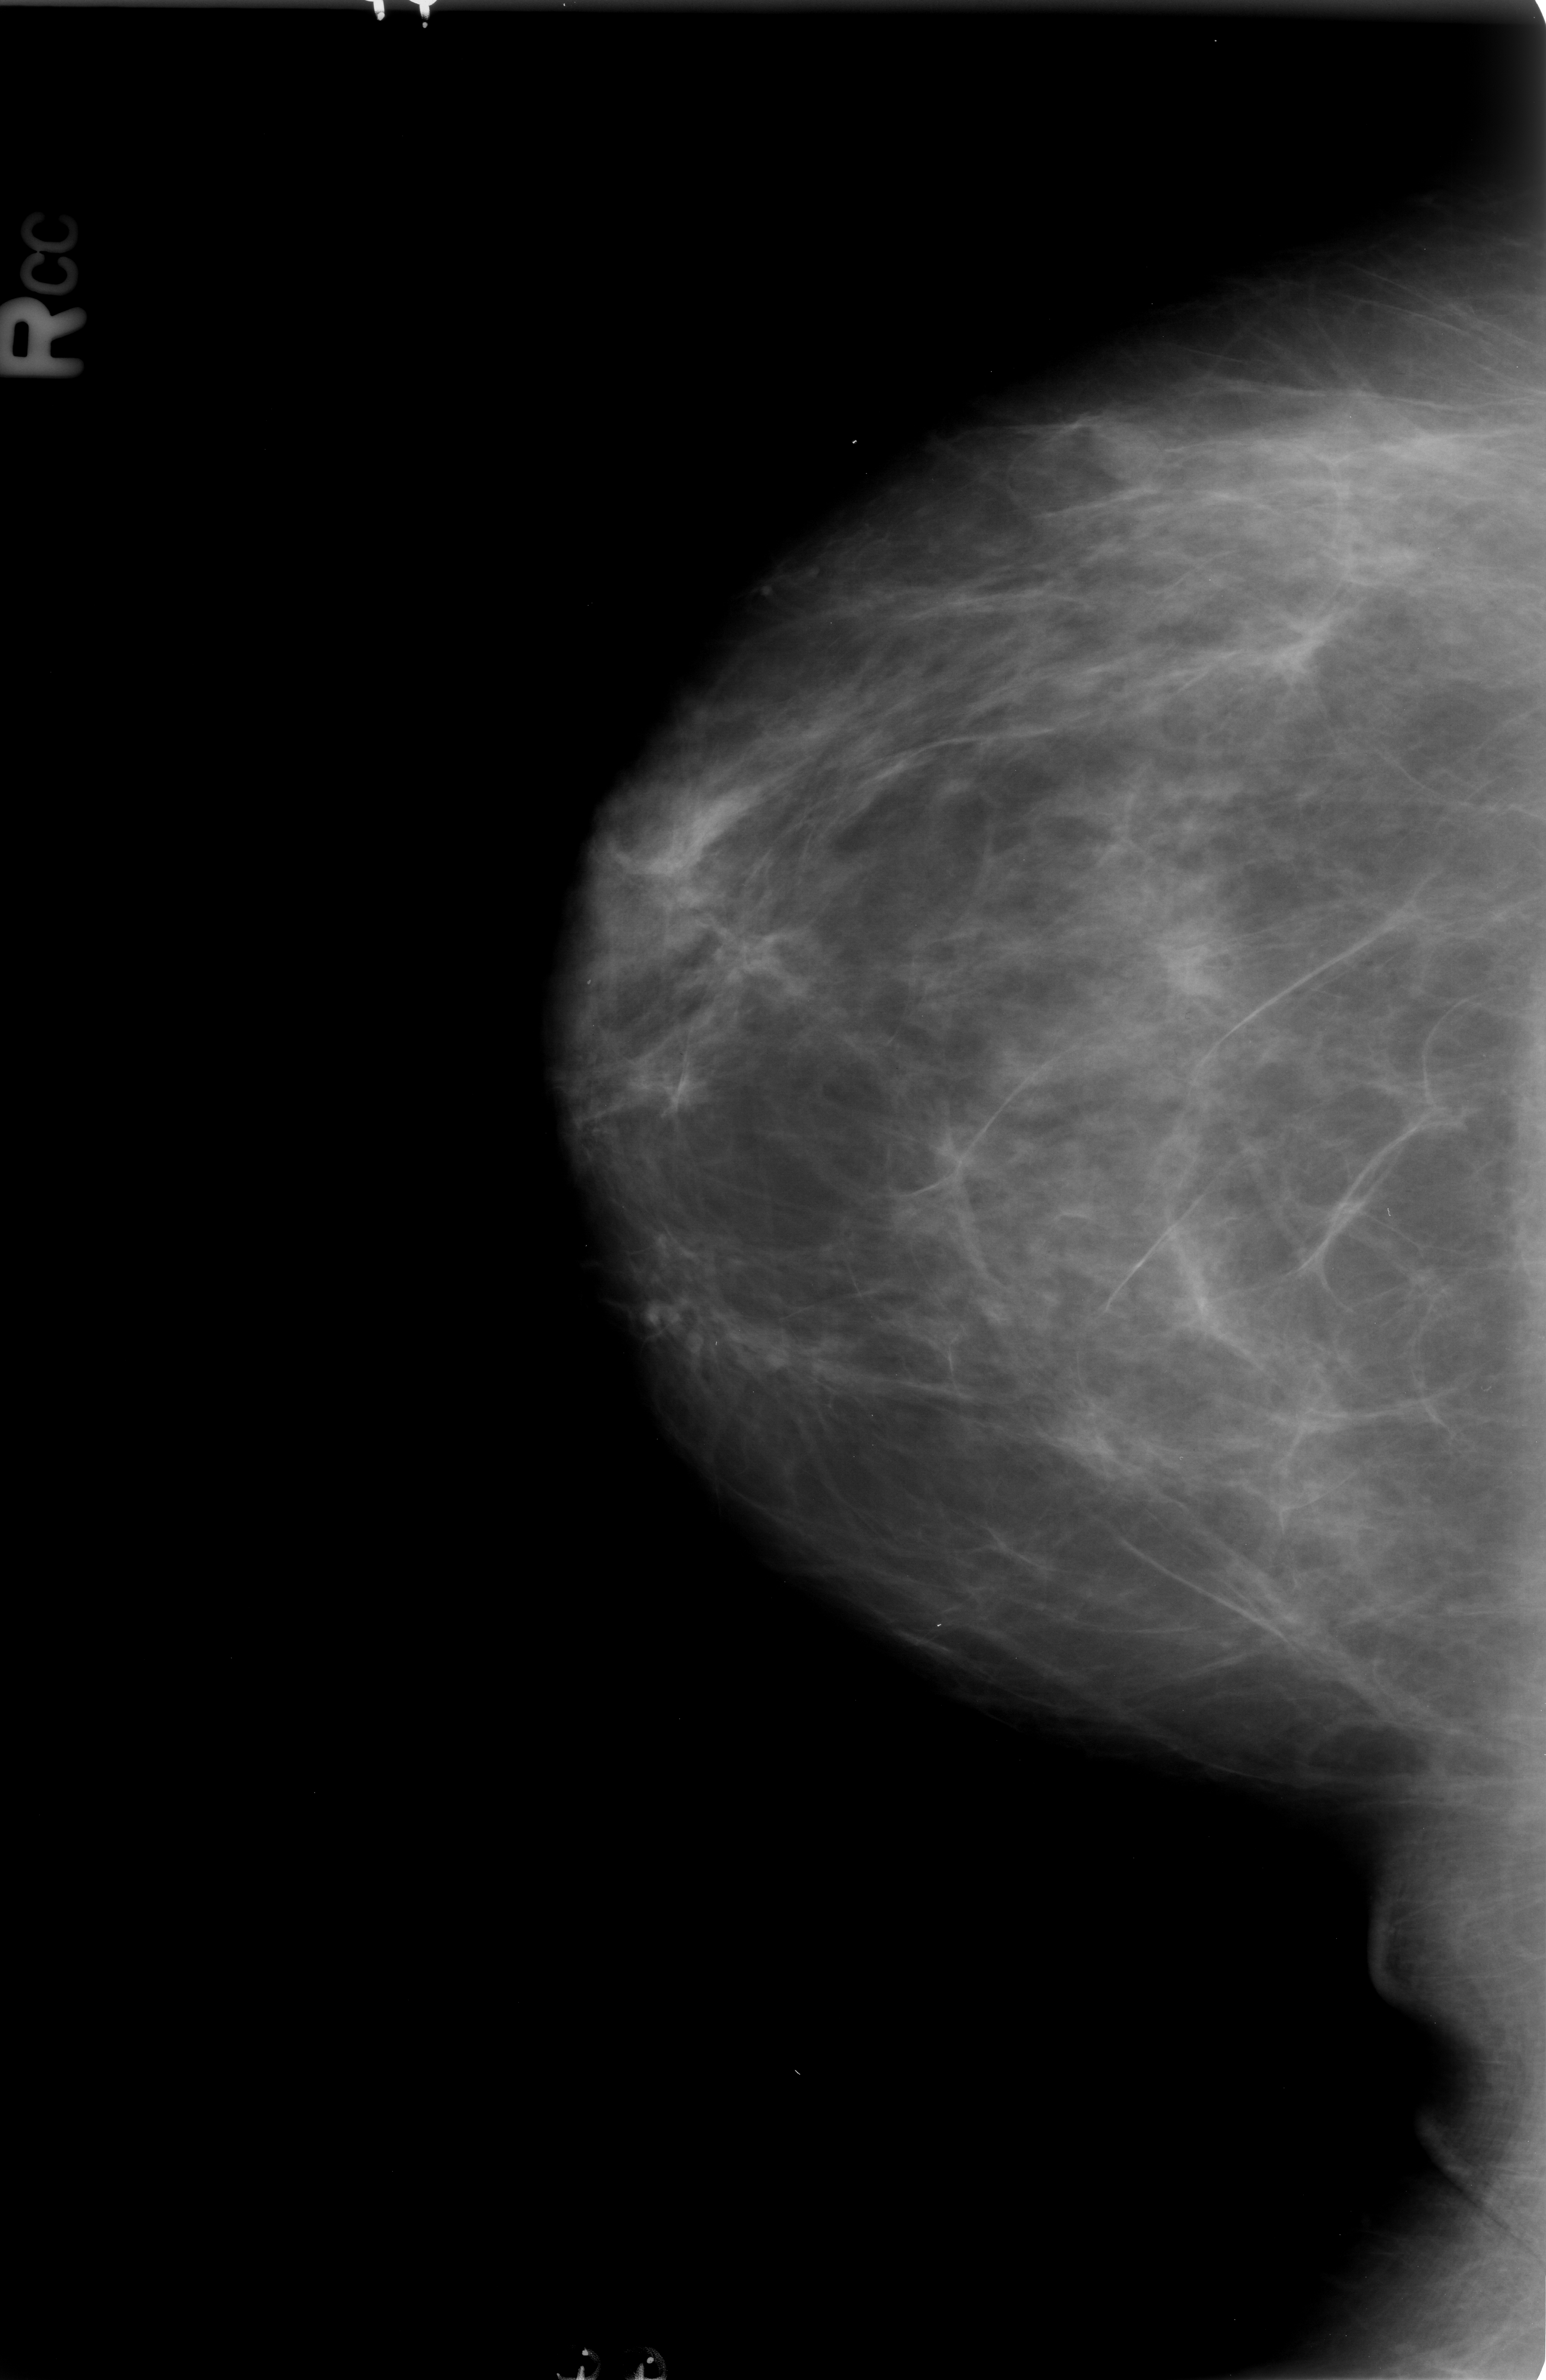
Digitized screen-film mammogram; right breast; CC view; BI-RADS breast density category 2 (scale 1–4).
- Mass, shape oval, margins circumscribed / obscured; BI-RADS assessment category 4; pathology (as recorded): benign.